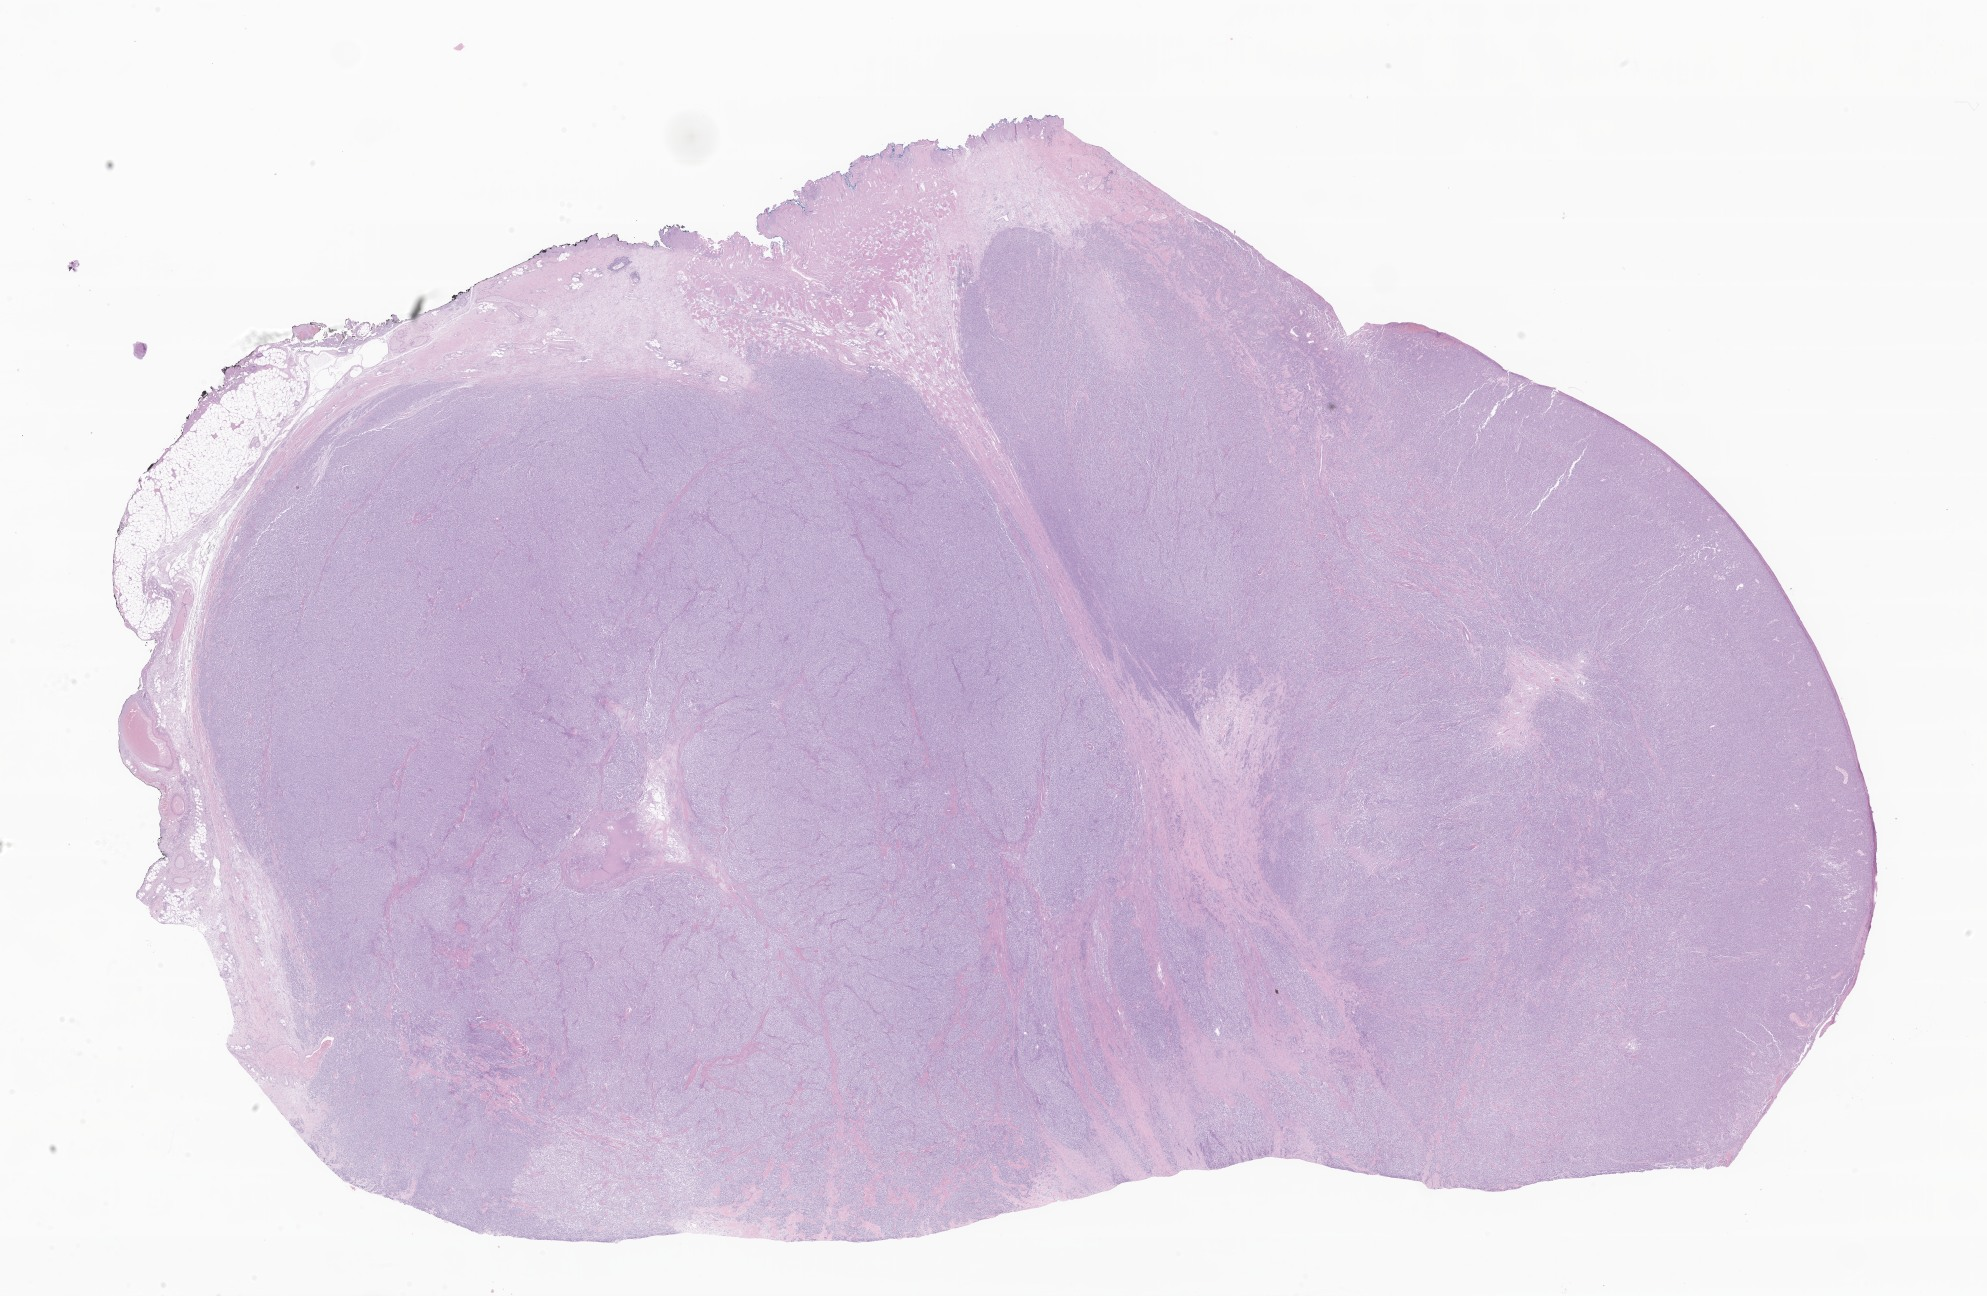
Whole-slide image, H&E stain of tumor tissue from the heart — a low-resolution overview of the entire scanned area, about 33.5 x 21.9 mm; formalin-fixed paraffin-embedded section. Patient male; age 152 months.
Diagnosis: Clear cell sarcoma, NOS.